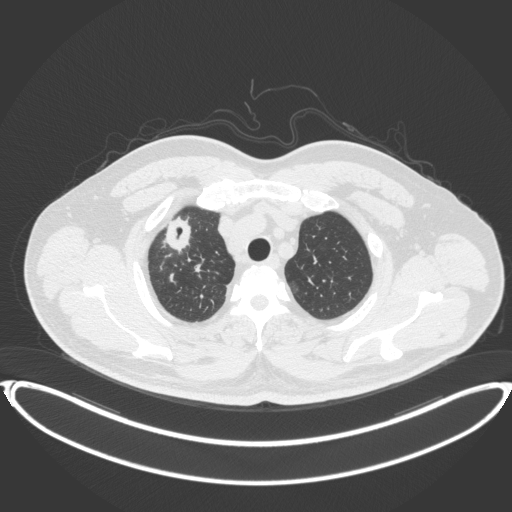
Chest CT, one axial slice; slice 330 of 399 in the series (ordered by position); reconstruction kernel B31f; 120 kVp; lung window (W 1500 / L -600 HU); 1 mm slice thickness; 512 × 512 image matrix, field of view 445 × 445 mm. Patient: male, 53 years. From the clinical record (not read from this slice): clinical TNM (as recorded): T2a N0 M0.
Annotated regions visible in this slice (bounding box drawn by a radiologist):
- lung tumour (recorded histology: adenocarcinoma): bounding box (x1, y1, x2, y2) in pixels: (164, 212, 198, 256)